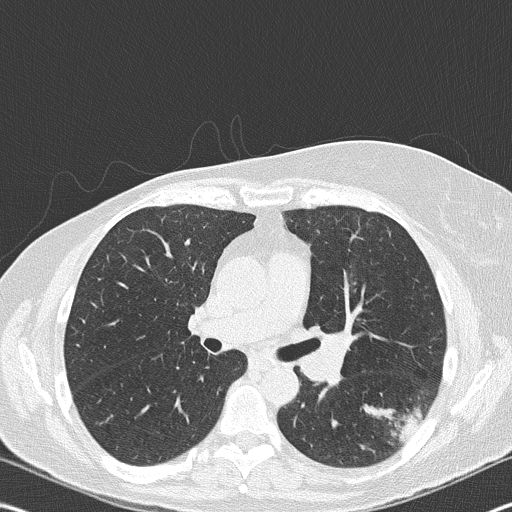
Low-dose screening chest CT, axial slice; second annual screen; lung window (W 1500 / L -600 HU); 2 mm slice thickness; lung (sharp) reconstruction kernel (B50f); slice 106 of 177 in the series; 512 × 512 image matrix. Female participant, aged 60 years at enrolment. Current smoker at enrolment.
• Lesion marked by an expert reader, bounding box <373,383,442,451> (left, top, right, bottom; pixels).
• Reader record for this screening exam (exam-level; its link to the box is not recorded): non-calcified nodule or mass ≥4 mm, left lower lobe, 18 × 16 mm, spiculated (stellate) margins, soft tissue attenuation, pre-existing on the prior screen: no.
• Official screen result: positive, other.
• Lung cancer was diagnosed 35 days after this screen: carcinoma, NOS, left hilum, stage IV (AJCC 6th edition), 45 mm at pathology.